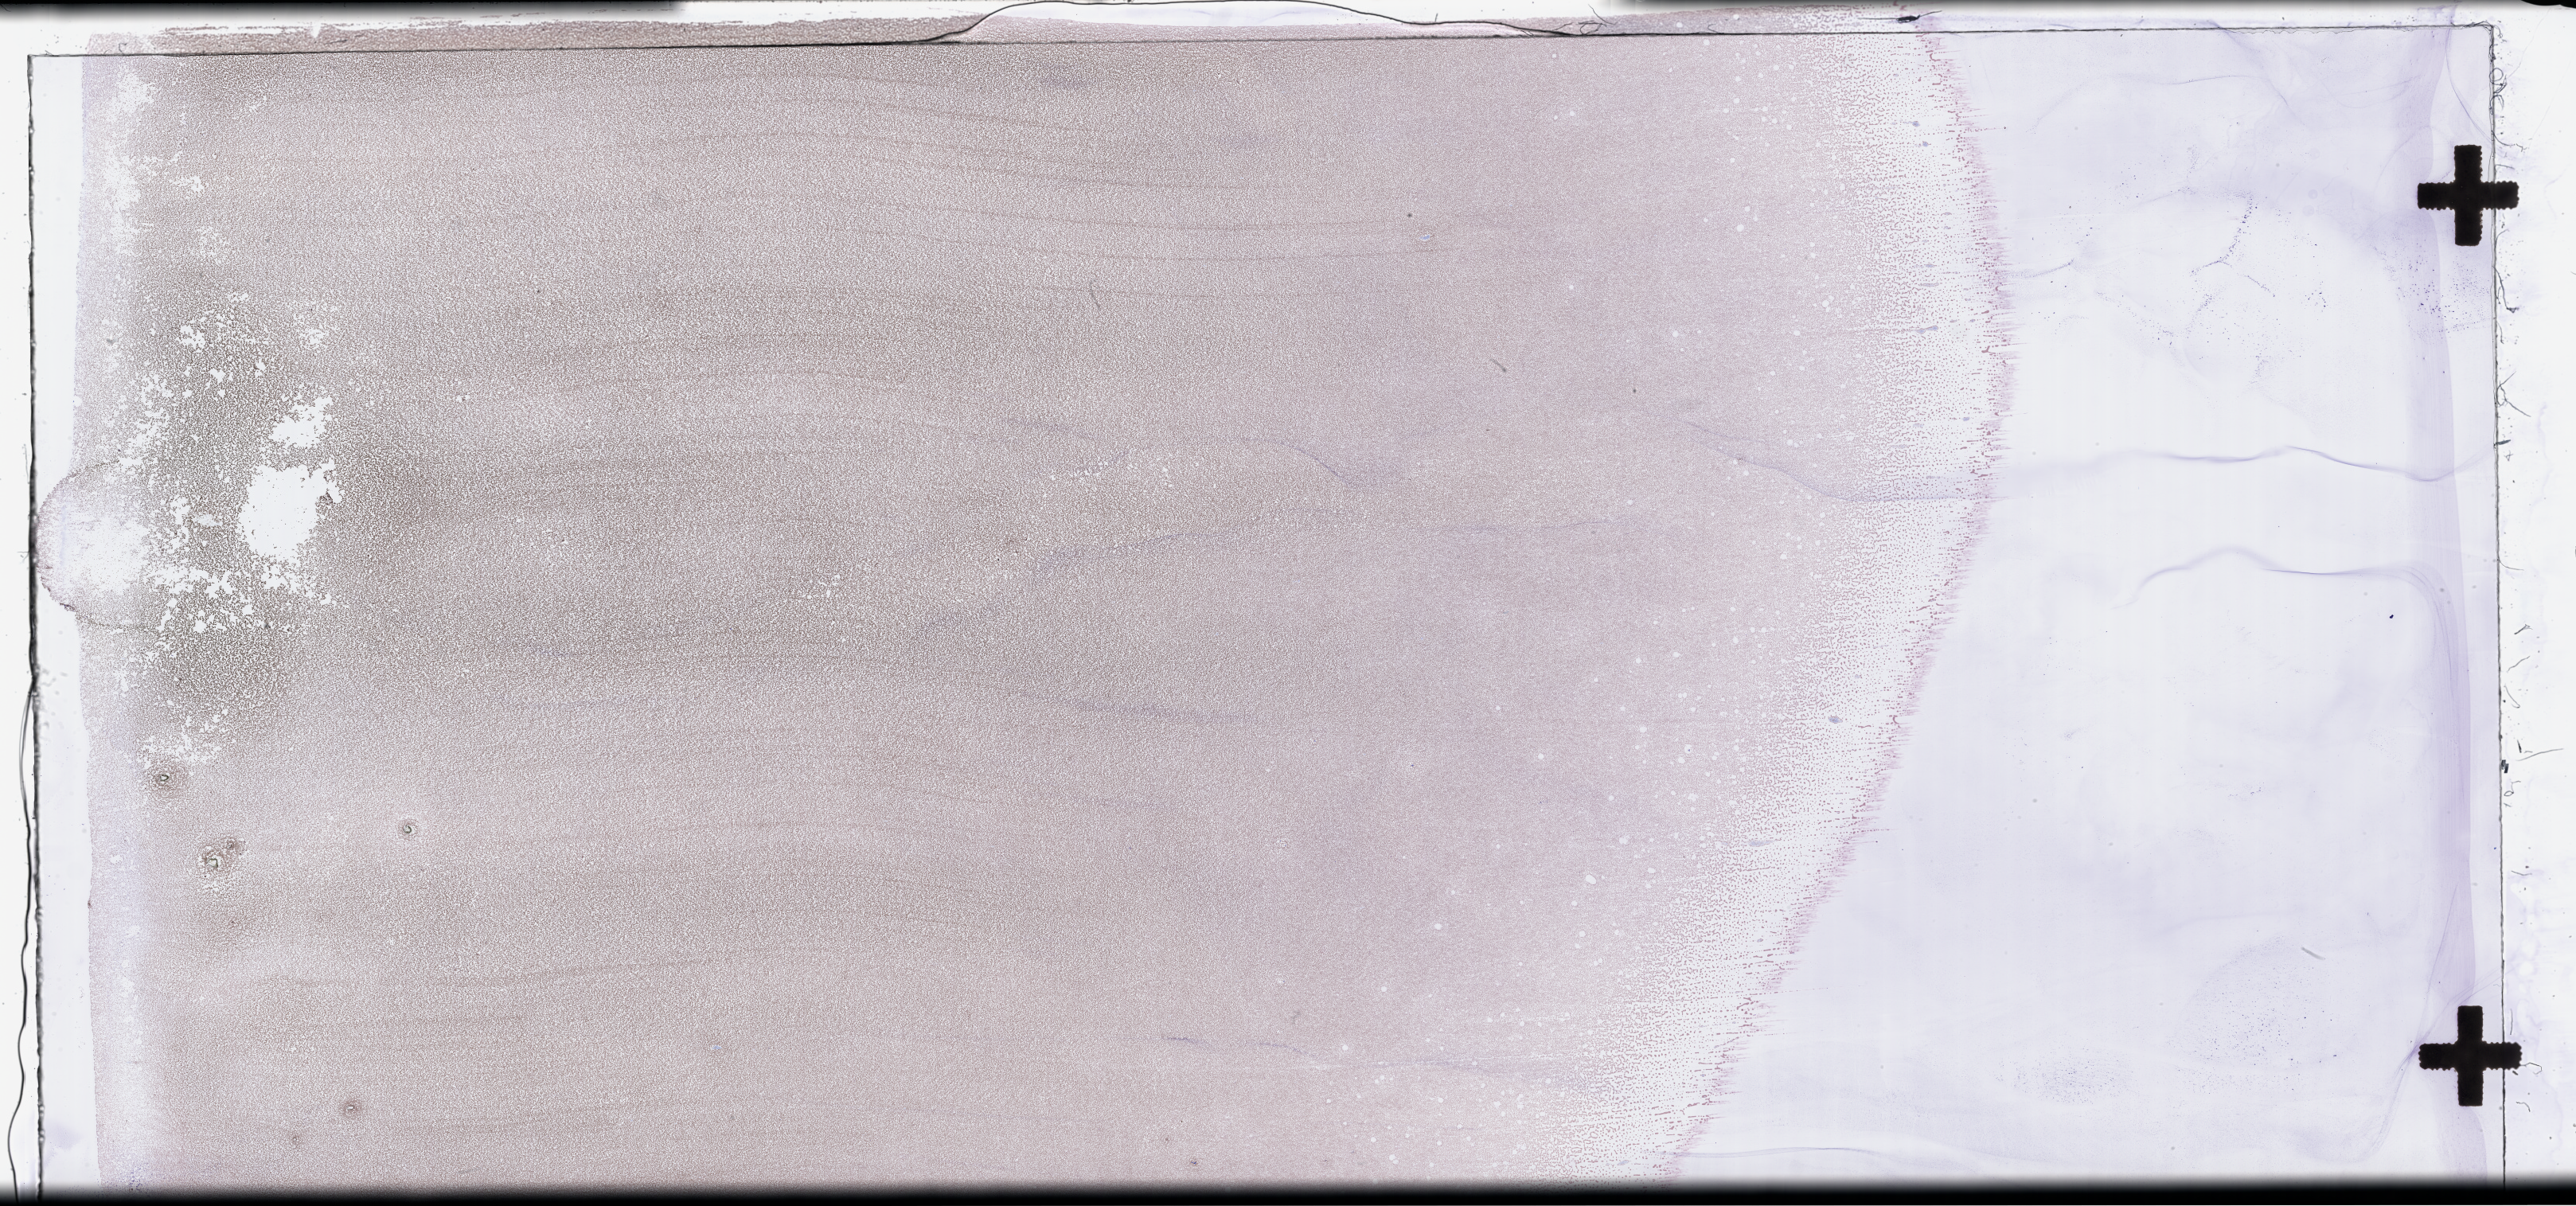
Whole-slide image of a whole blood smear, Wright-Giemsa stain — low-resolution overview of the scanned area, about 52.3 x 24.5 mm, smear from an EDTA sample, collected at baseline (before treatment). Patient: female.
Patient diagnosis: Acute Myeloid Leukemia Not Otherwise Specified.